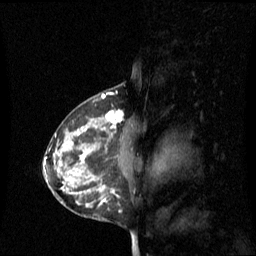
Breast MRI (dynamic contrast-enhanced), one sagittal slice; position 39 of 60 along the scan axis; dynamic contrast-enhanced series, image 2 of 3 at this slice position (ordered by acquisition); 1.5 T; TE 4.2 ms, TR 8.4 ms; 256 × 256 image matrix, field of view 240 × 240 mm. Patient: female, 42 years. From the clinical record (not read from this slice): setting: breast cancer imaged before/during neoadjuvant chemotherapy; receptor status: HR-positive, HER2-negative.
Annotated regions visible in this slice (semi-automatic segmentation, software-assisted and operator-edited):
- analysis volume of interest (the breast-tissue region the enhancement analysis was run in; not a lesion): bounding box [x1, y1, x2, y2] px = [68, 110, 137, 201]
- tumour enhancement mask (voxels above the 70 % enhancement threshold inside the analysis volume of interest): [80, 110, 123, 201]